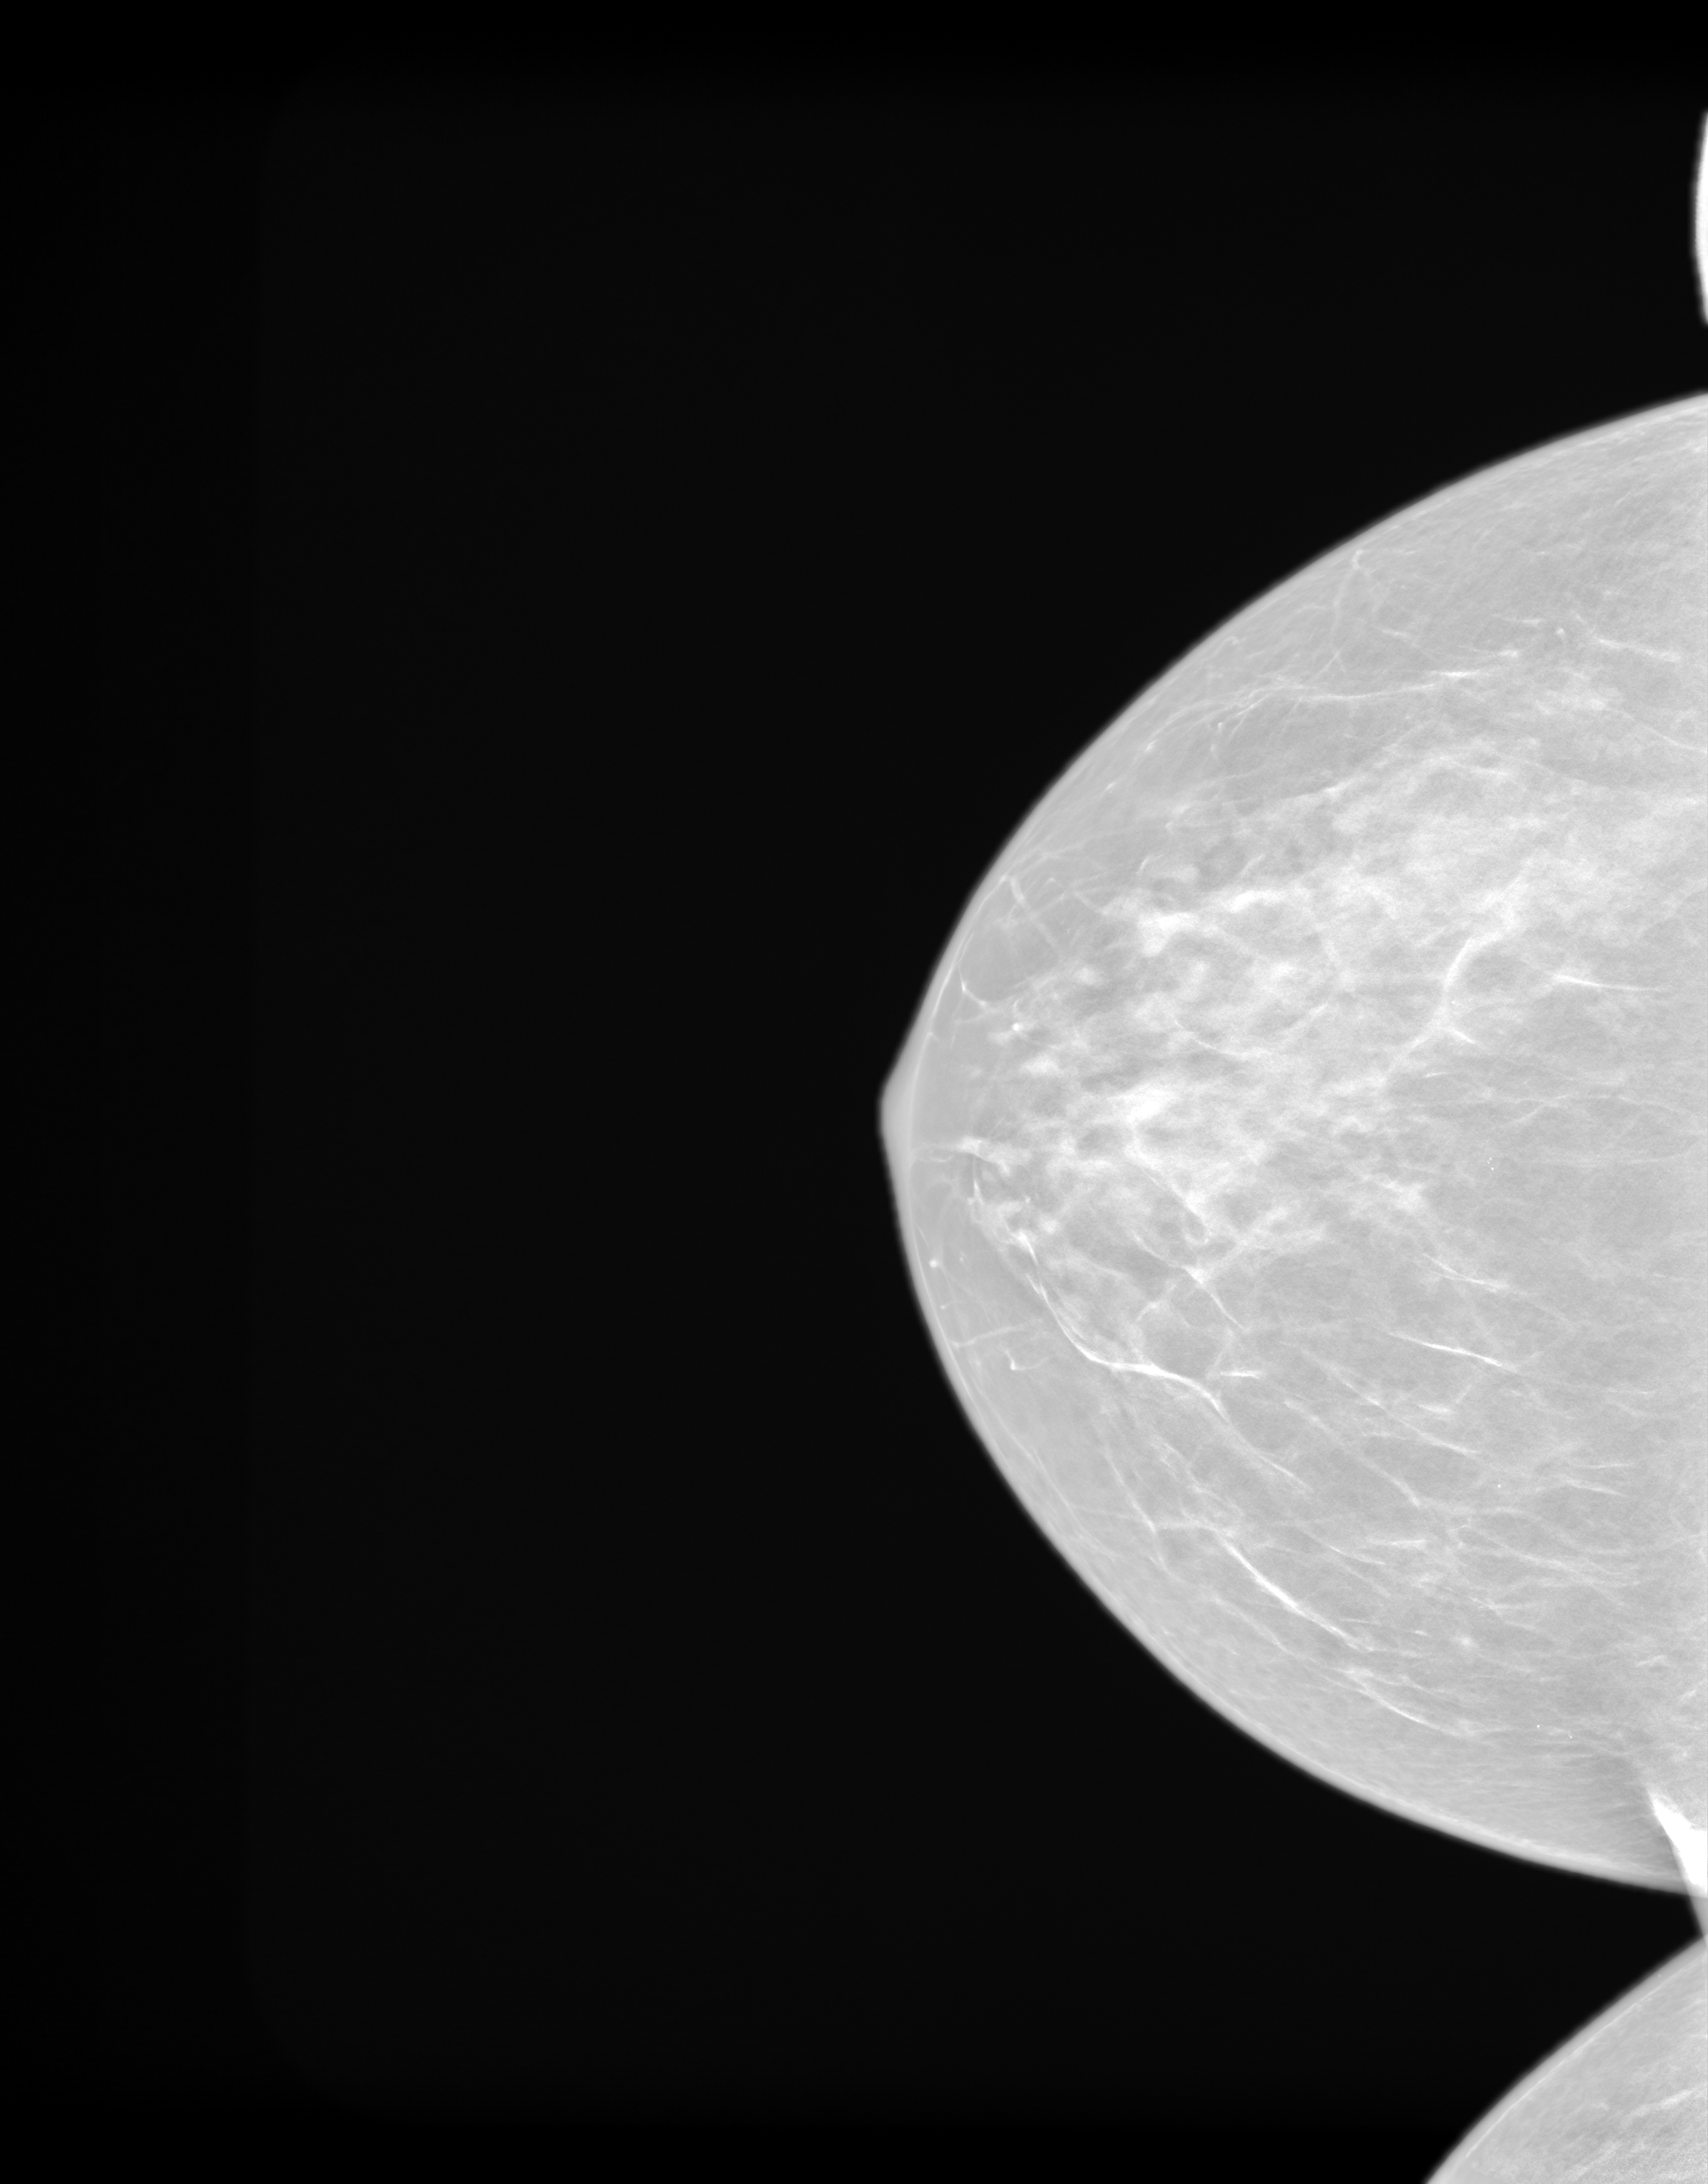
Synthetic 2-D view generated from a tomosynthesis acquisition (not an FFDM exposure), right breast, cranio-caudal projection, annual screening mammography examination, system: SenoIris_1SP1.1(421). Female patient, age 57 years.
Final BI-RADS assessment for this screening round (tomosynthesis exam, both breasts): category 1.